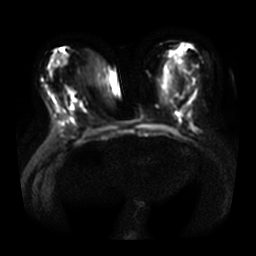
Breast MRI, one axial slice. Slice 14 of 33 in the series (ordered by position). Diffusion-weighted series; image 2 of 4 stored at this slice position (different b-values; order by instance number). 3 T. 5 mm slice thickness. 256 × 256 image matrix, field of view 360 × 360 mm. Female patient.
Outlined on this slice (expert manual segmentation):
- tumour on diffusion-weighted imaging: box from (x=67, y=89) to (x=75, y=96) px